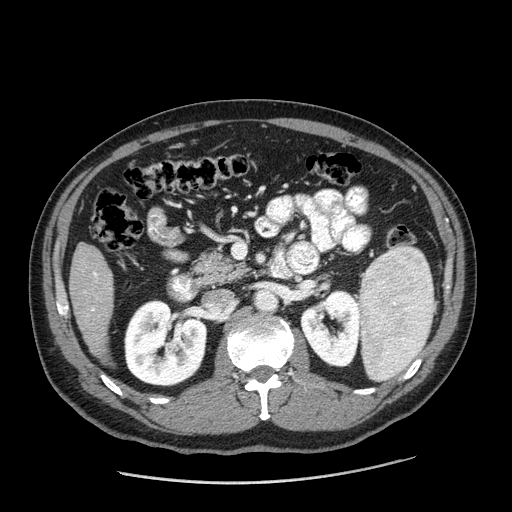
Contrast-enhanced abdominal CT (liver protocol), one axial slice; position 65 of 198 along the scan axis; 120 kVp; one of 2 acquisitions stored at this slice position; soft-tissue window (W 400 / L 40 HU); 512 × 512 image matrix, field of view 400 × 400 mm. From the clinical record (not read from this slice): diagnosis: hepatocellular carcinoma (patient treated with transarterial chemoembolisation; whether this scan precedes or follows treatment is not stated here); TNM stage (as recorded): Stage-II; Child-Pugh class: A; tumour differentiation: moderately differentiated; tumour nodularity: multinodular.
Structures marked on this image (semi-automatically segmented with operator editing):
- liver parenchyma outside the tumour (the mass and vessels are separate outlines, so this box may not span the whole liver): bounding box <68,242,114,358> (left, top, right, bottom; pixels)
- liver vessels: <92,272,98,311>